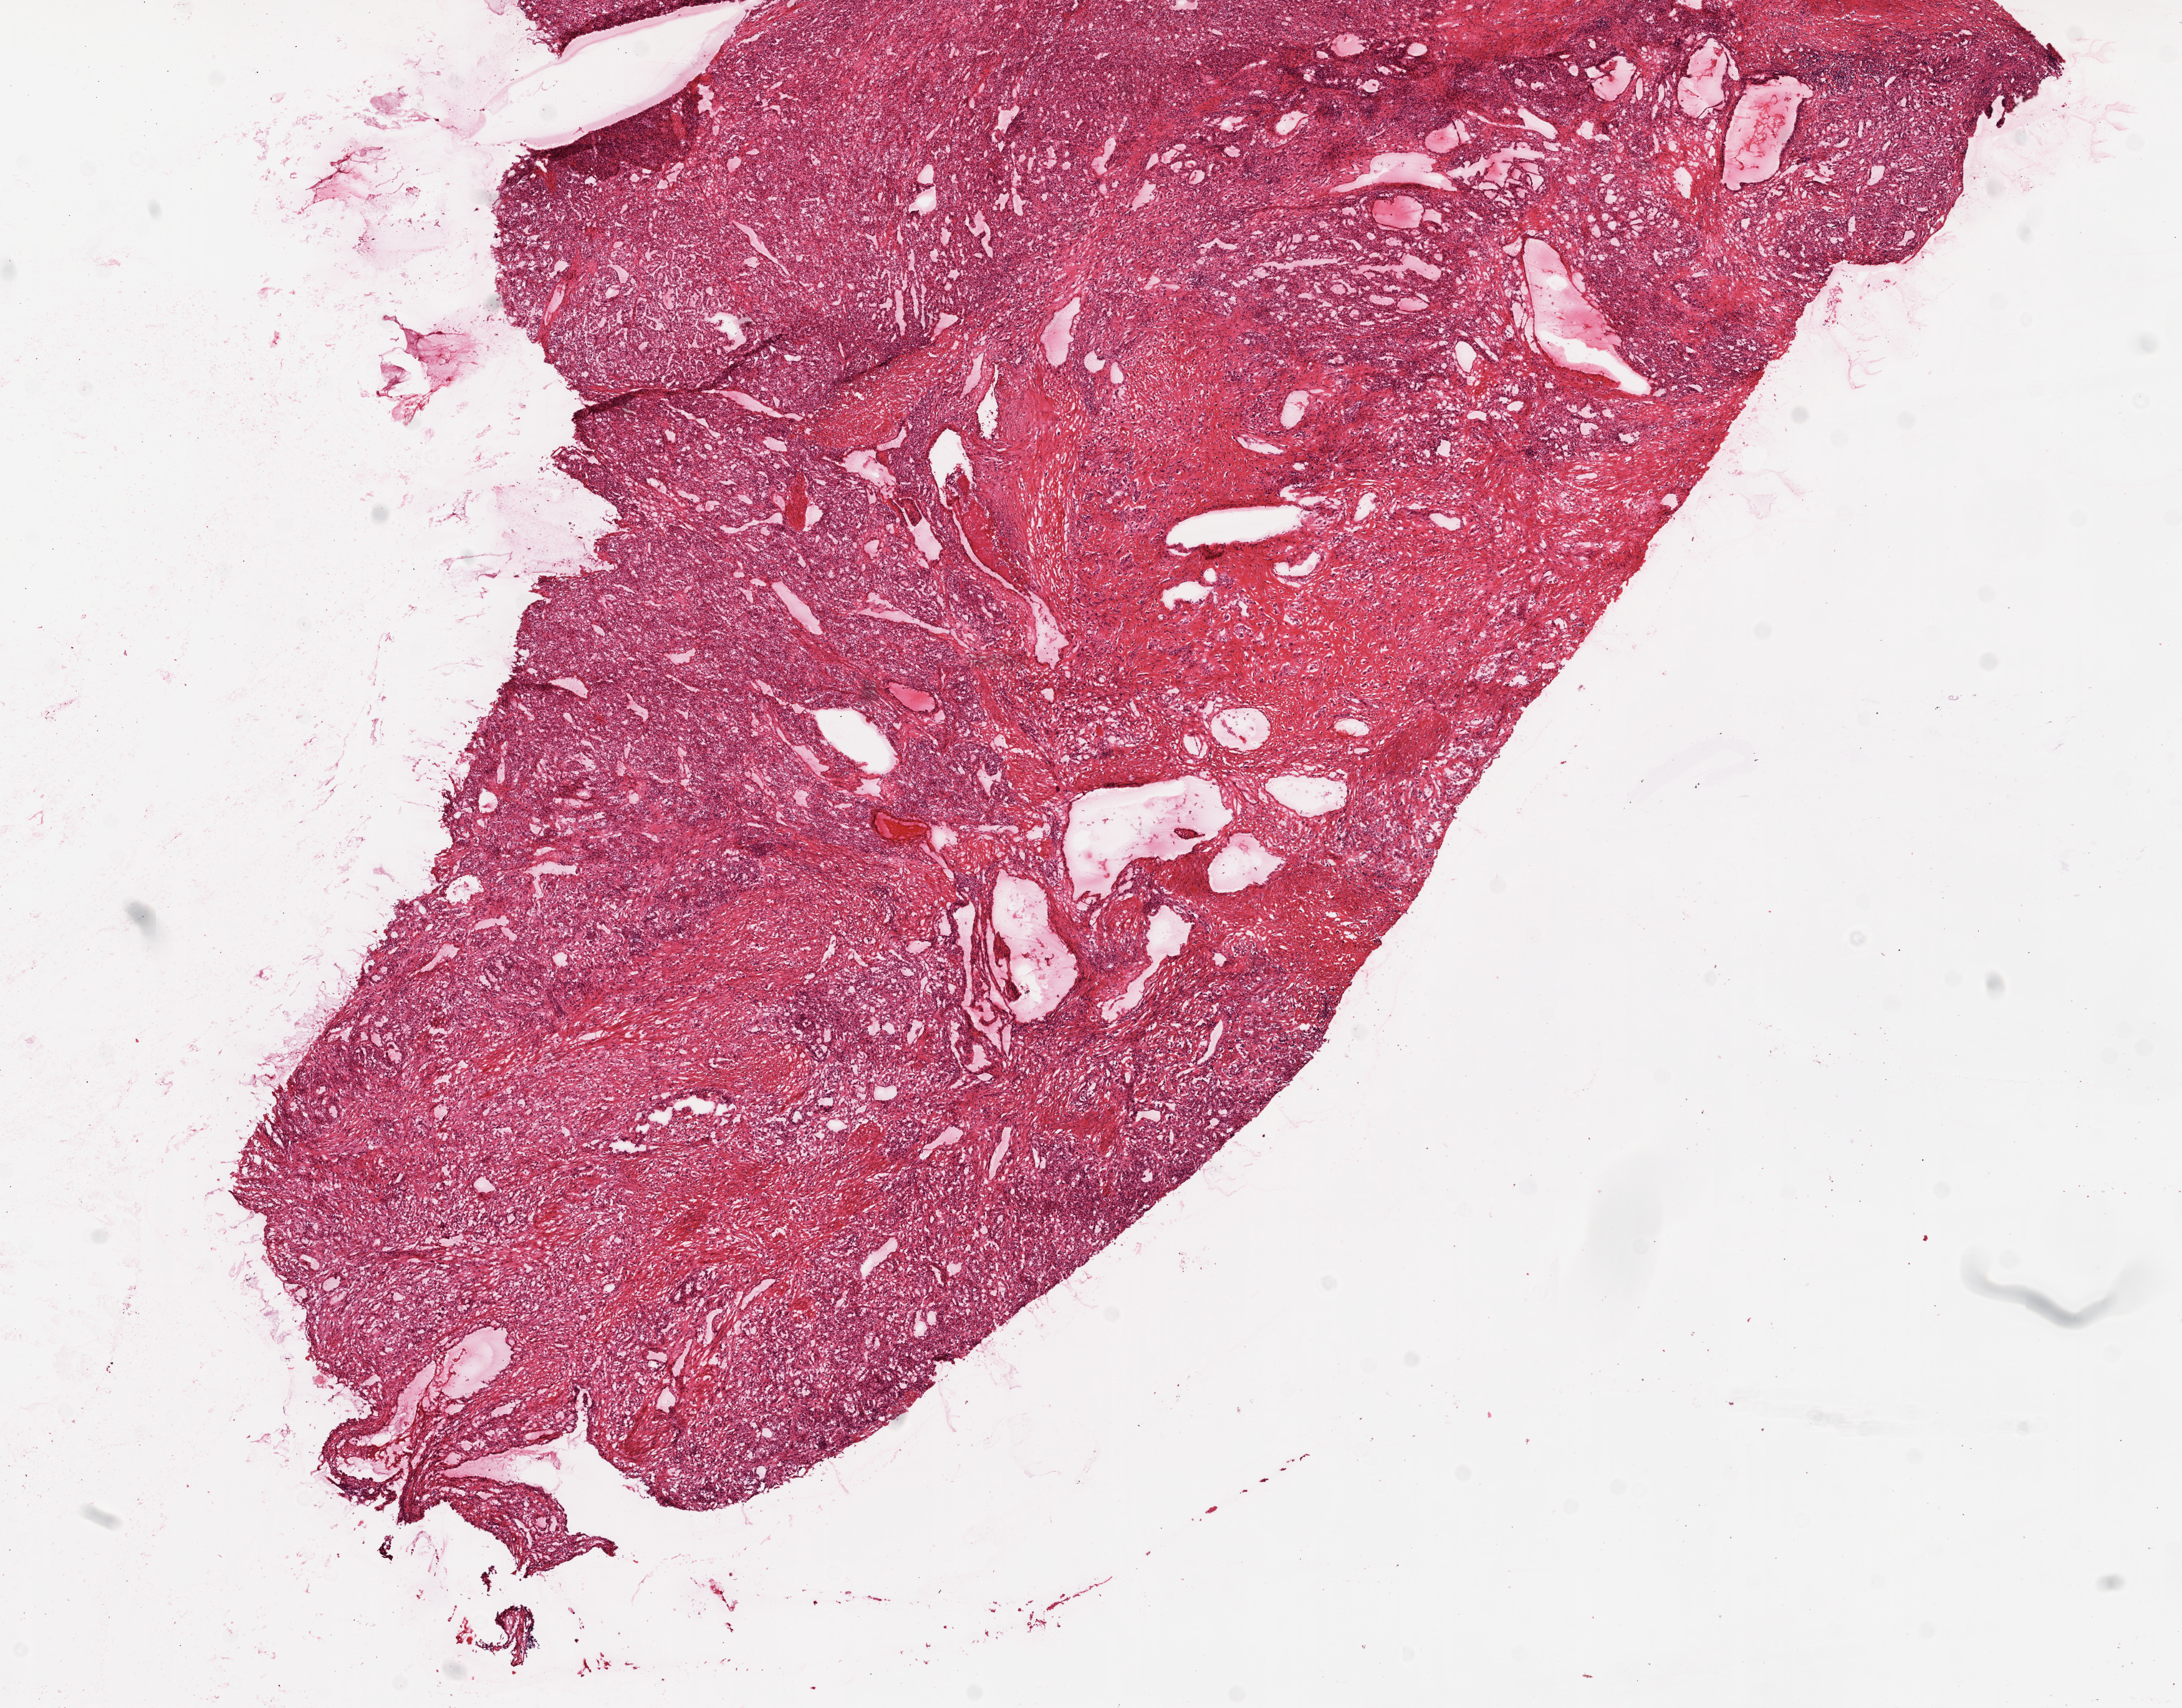
Whole-slide histology image, H&E-stained — a low-resolution overview of the entire scanned area, about 14.0 x 11.0 mm. Frozen section from the top of the tissue portion. Primary tumour sample from the kidney. Male patient; age at initial diagnosis 47 years. Composition of this section per pathologist review: tumour cells 85%, tumour nuclei 80%.
Diagnosis: Clear cell adenocarcinoma, NOS.